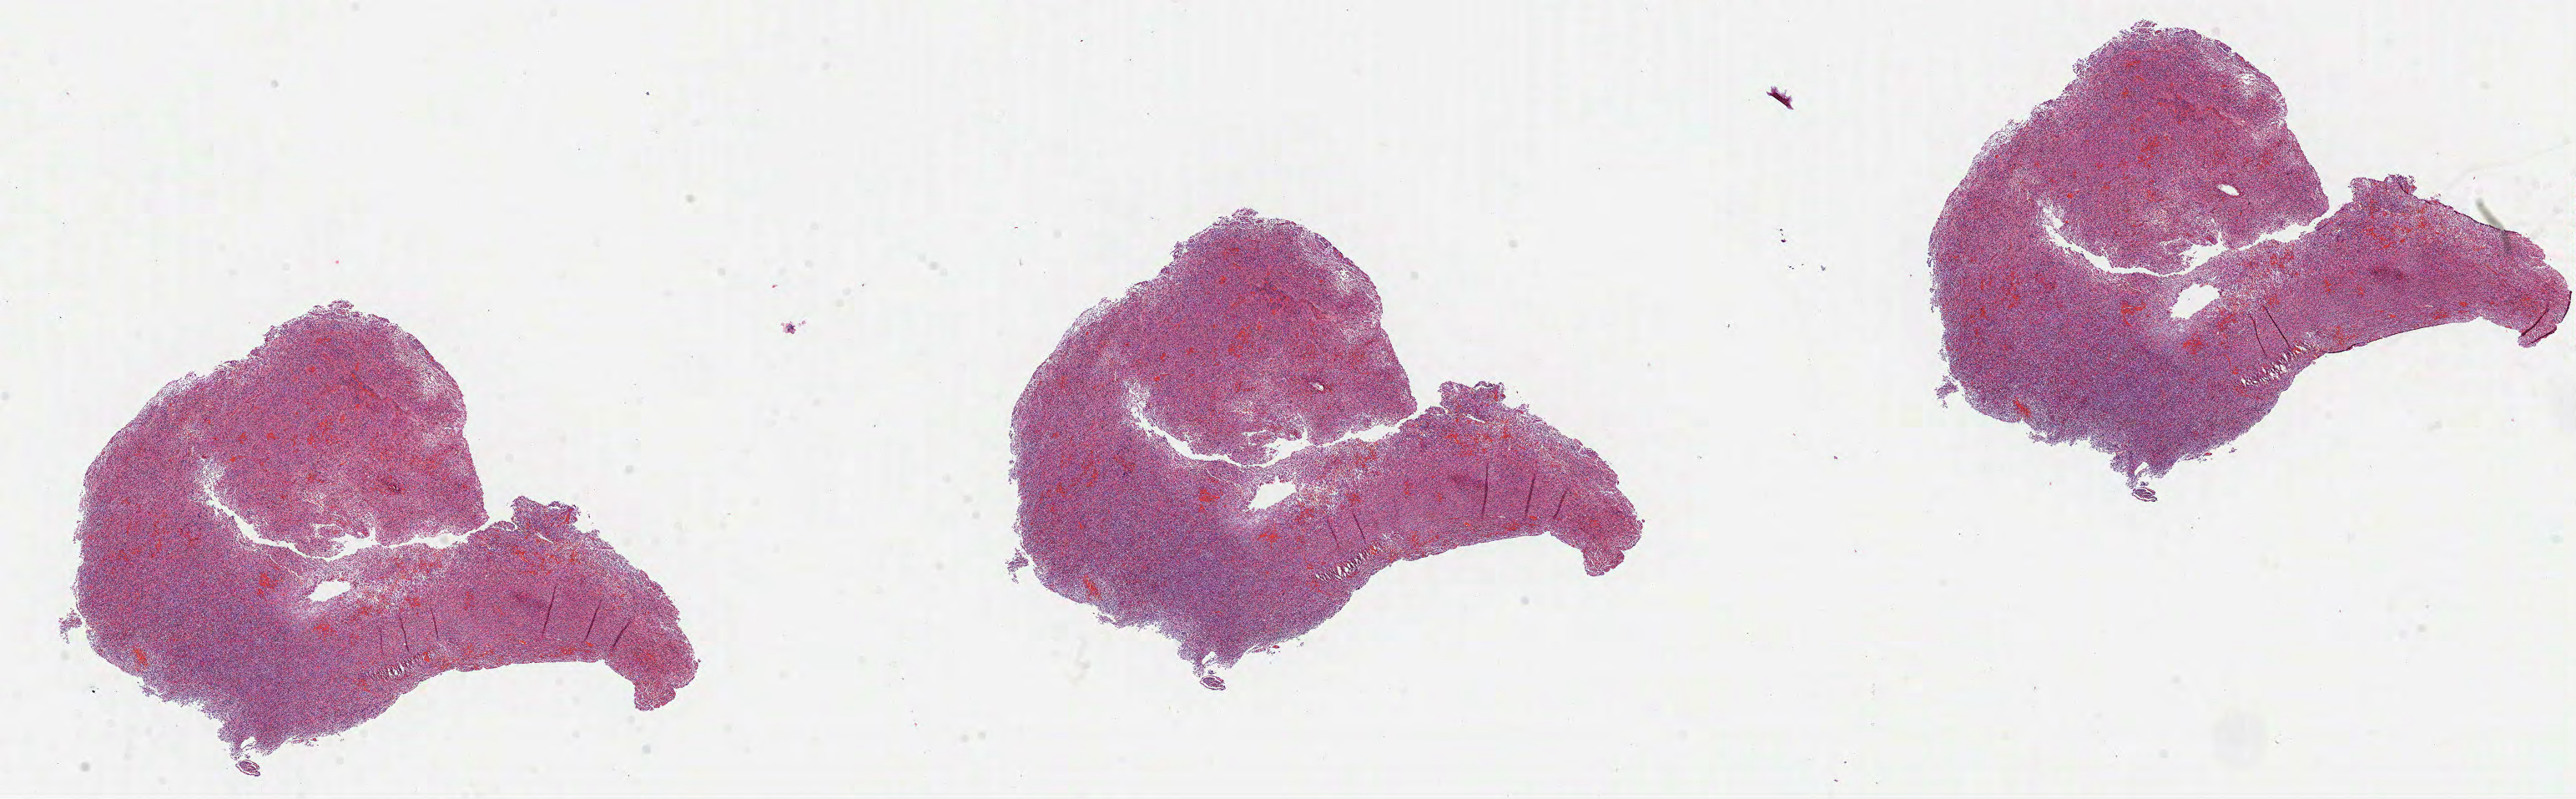
Whole-slide histology image, H&E-stained — low-resolution overview of the scanned area, about 24.9 x 7.7 mm (acquisition: 40x scan); formalin-fixed paraffin-embedded (FFPE) diagnostic section; brain, primary tumour sample. Patient: male, age at initial diagnosis 67 years.
Pathologic diagnosis: Glioblastoma.